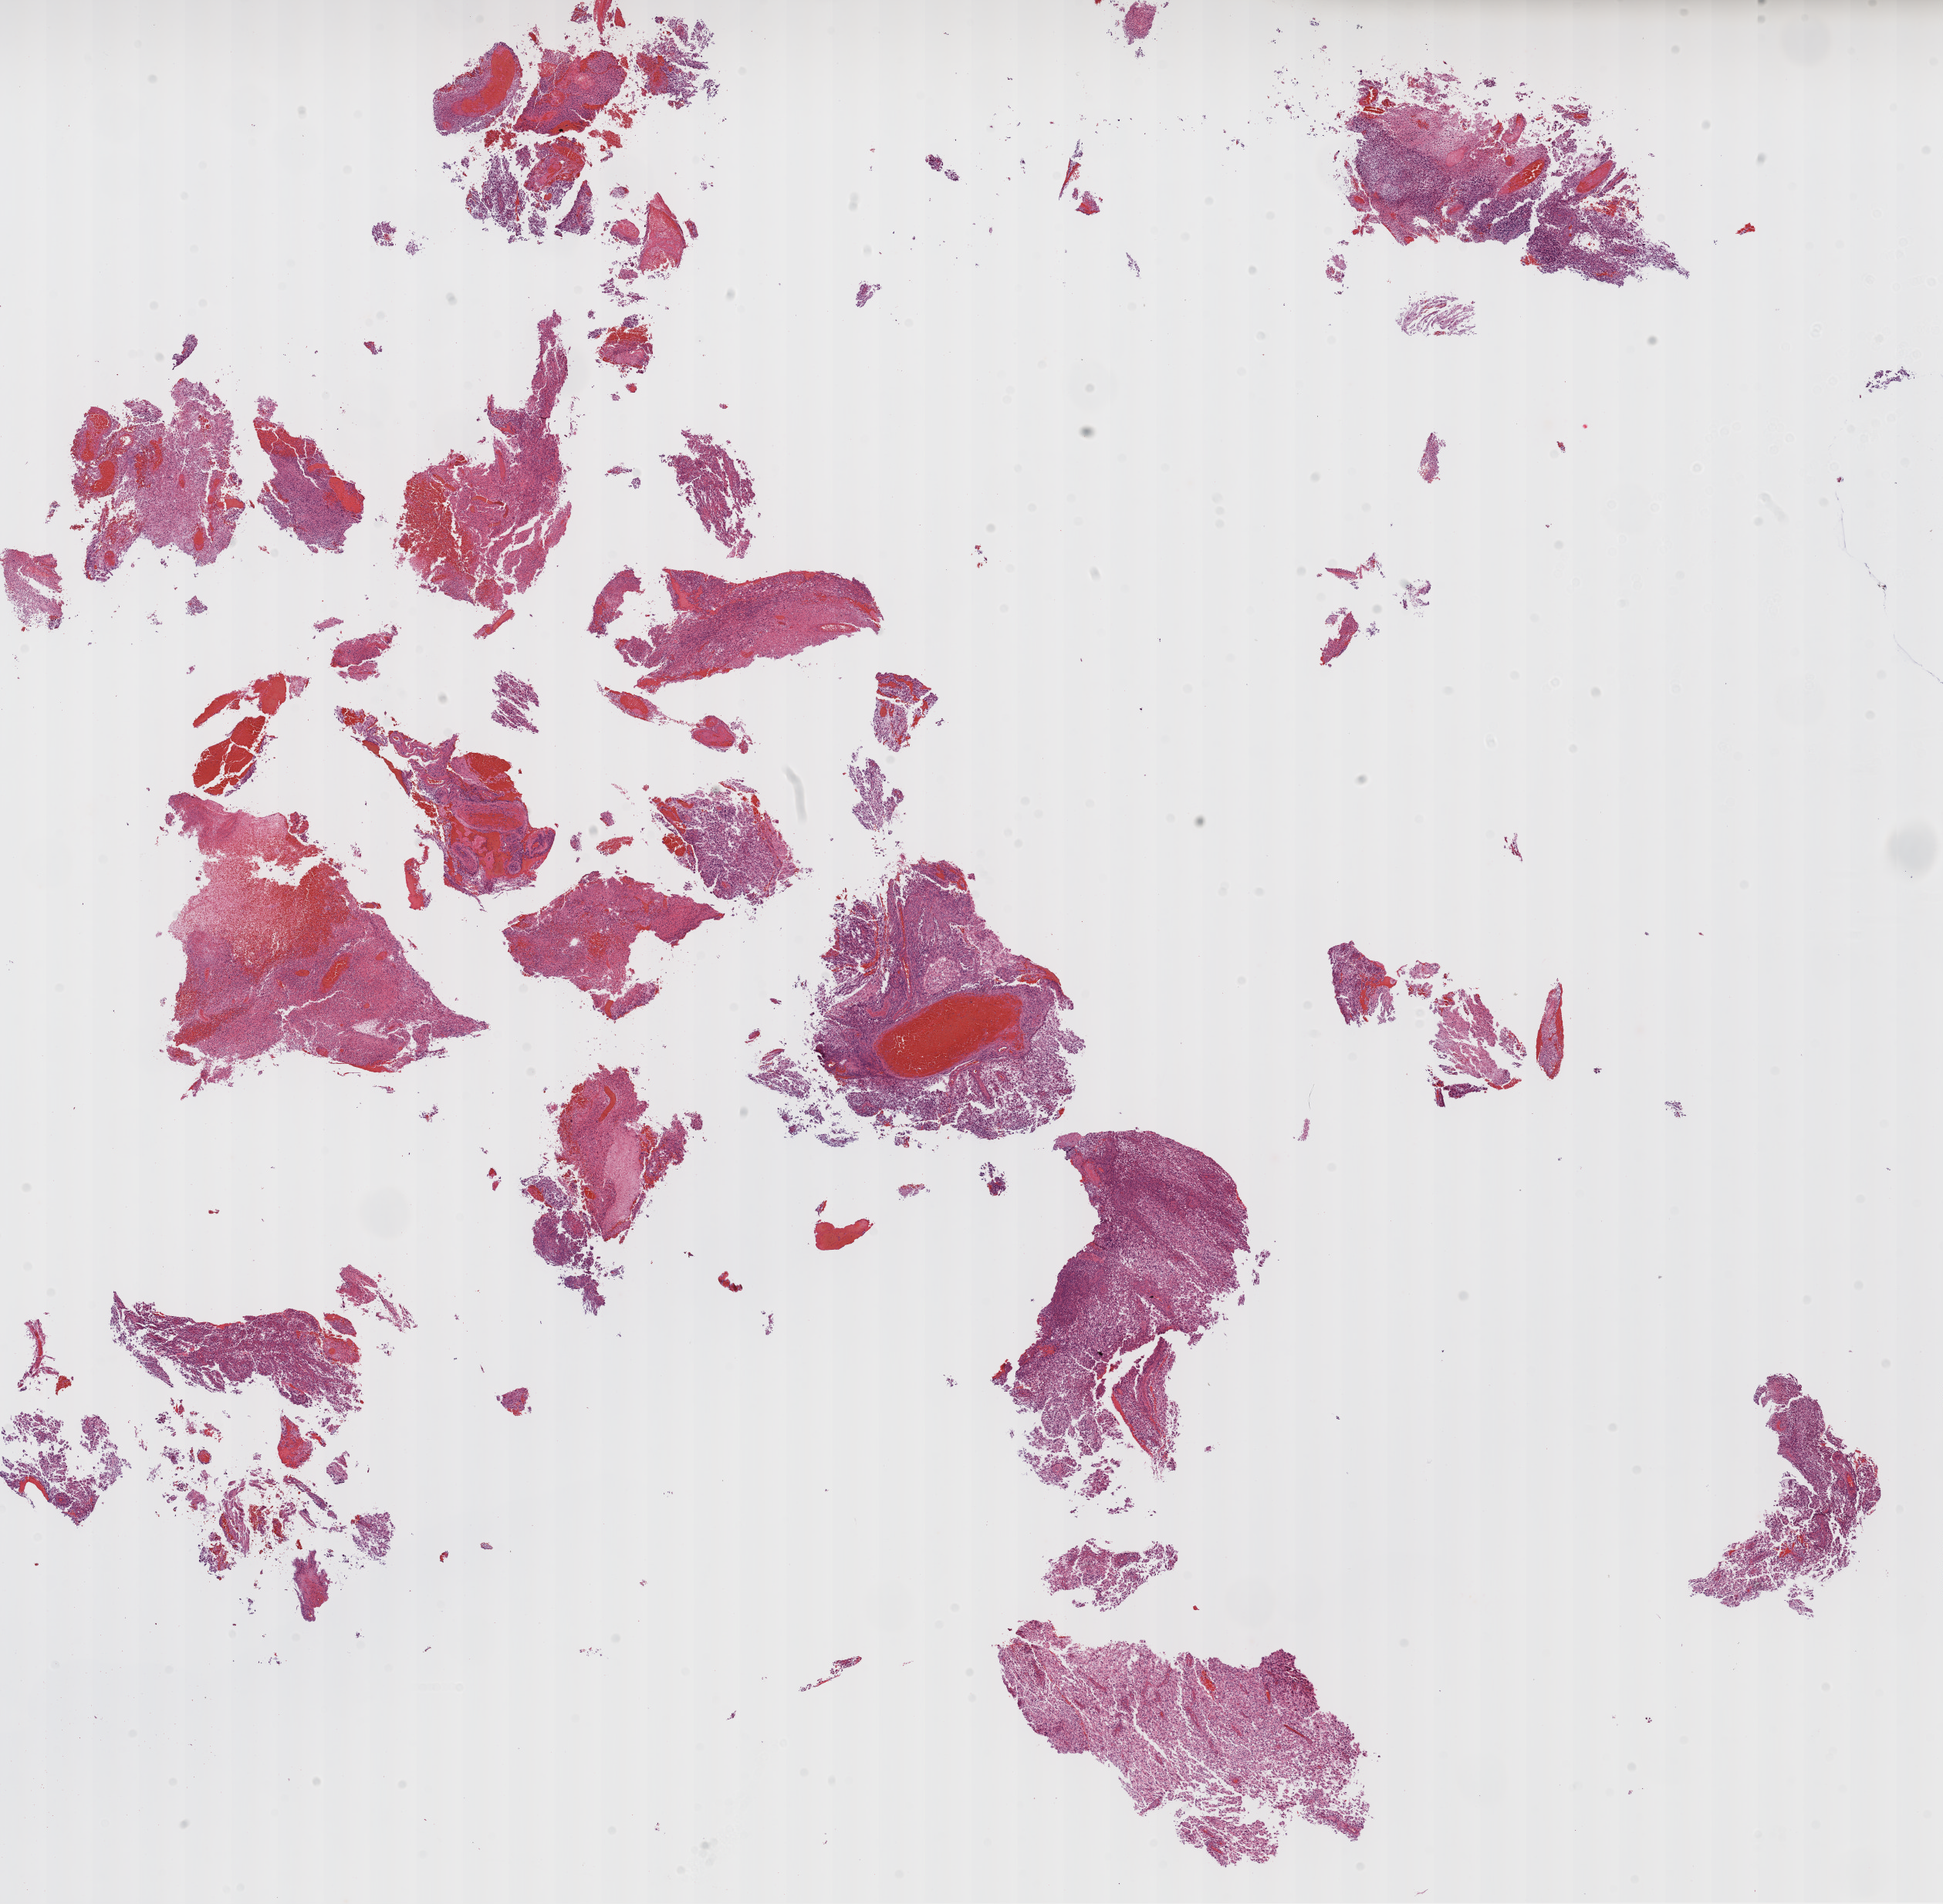
Whole-slide histology image, Hematoxylin and eosin (H&E) stained — whole scanned area (about 20.3 x 19.9 mm, from a 20x scan) shown as a low-resolution overview. Formalin-fixed paraffin-embedded (FFPE) diagnostic section. Sample: primary tumour, brain. Male, age 57 years at initial diagnosis.
• diagnosis: Glioblastoma